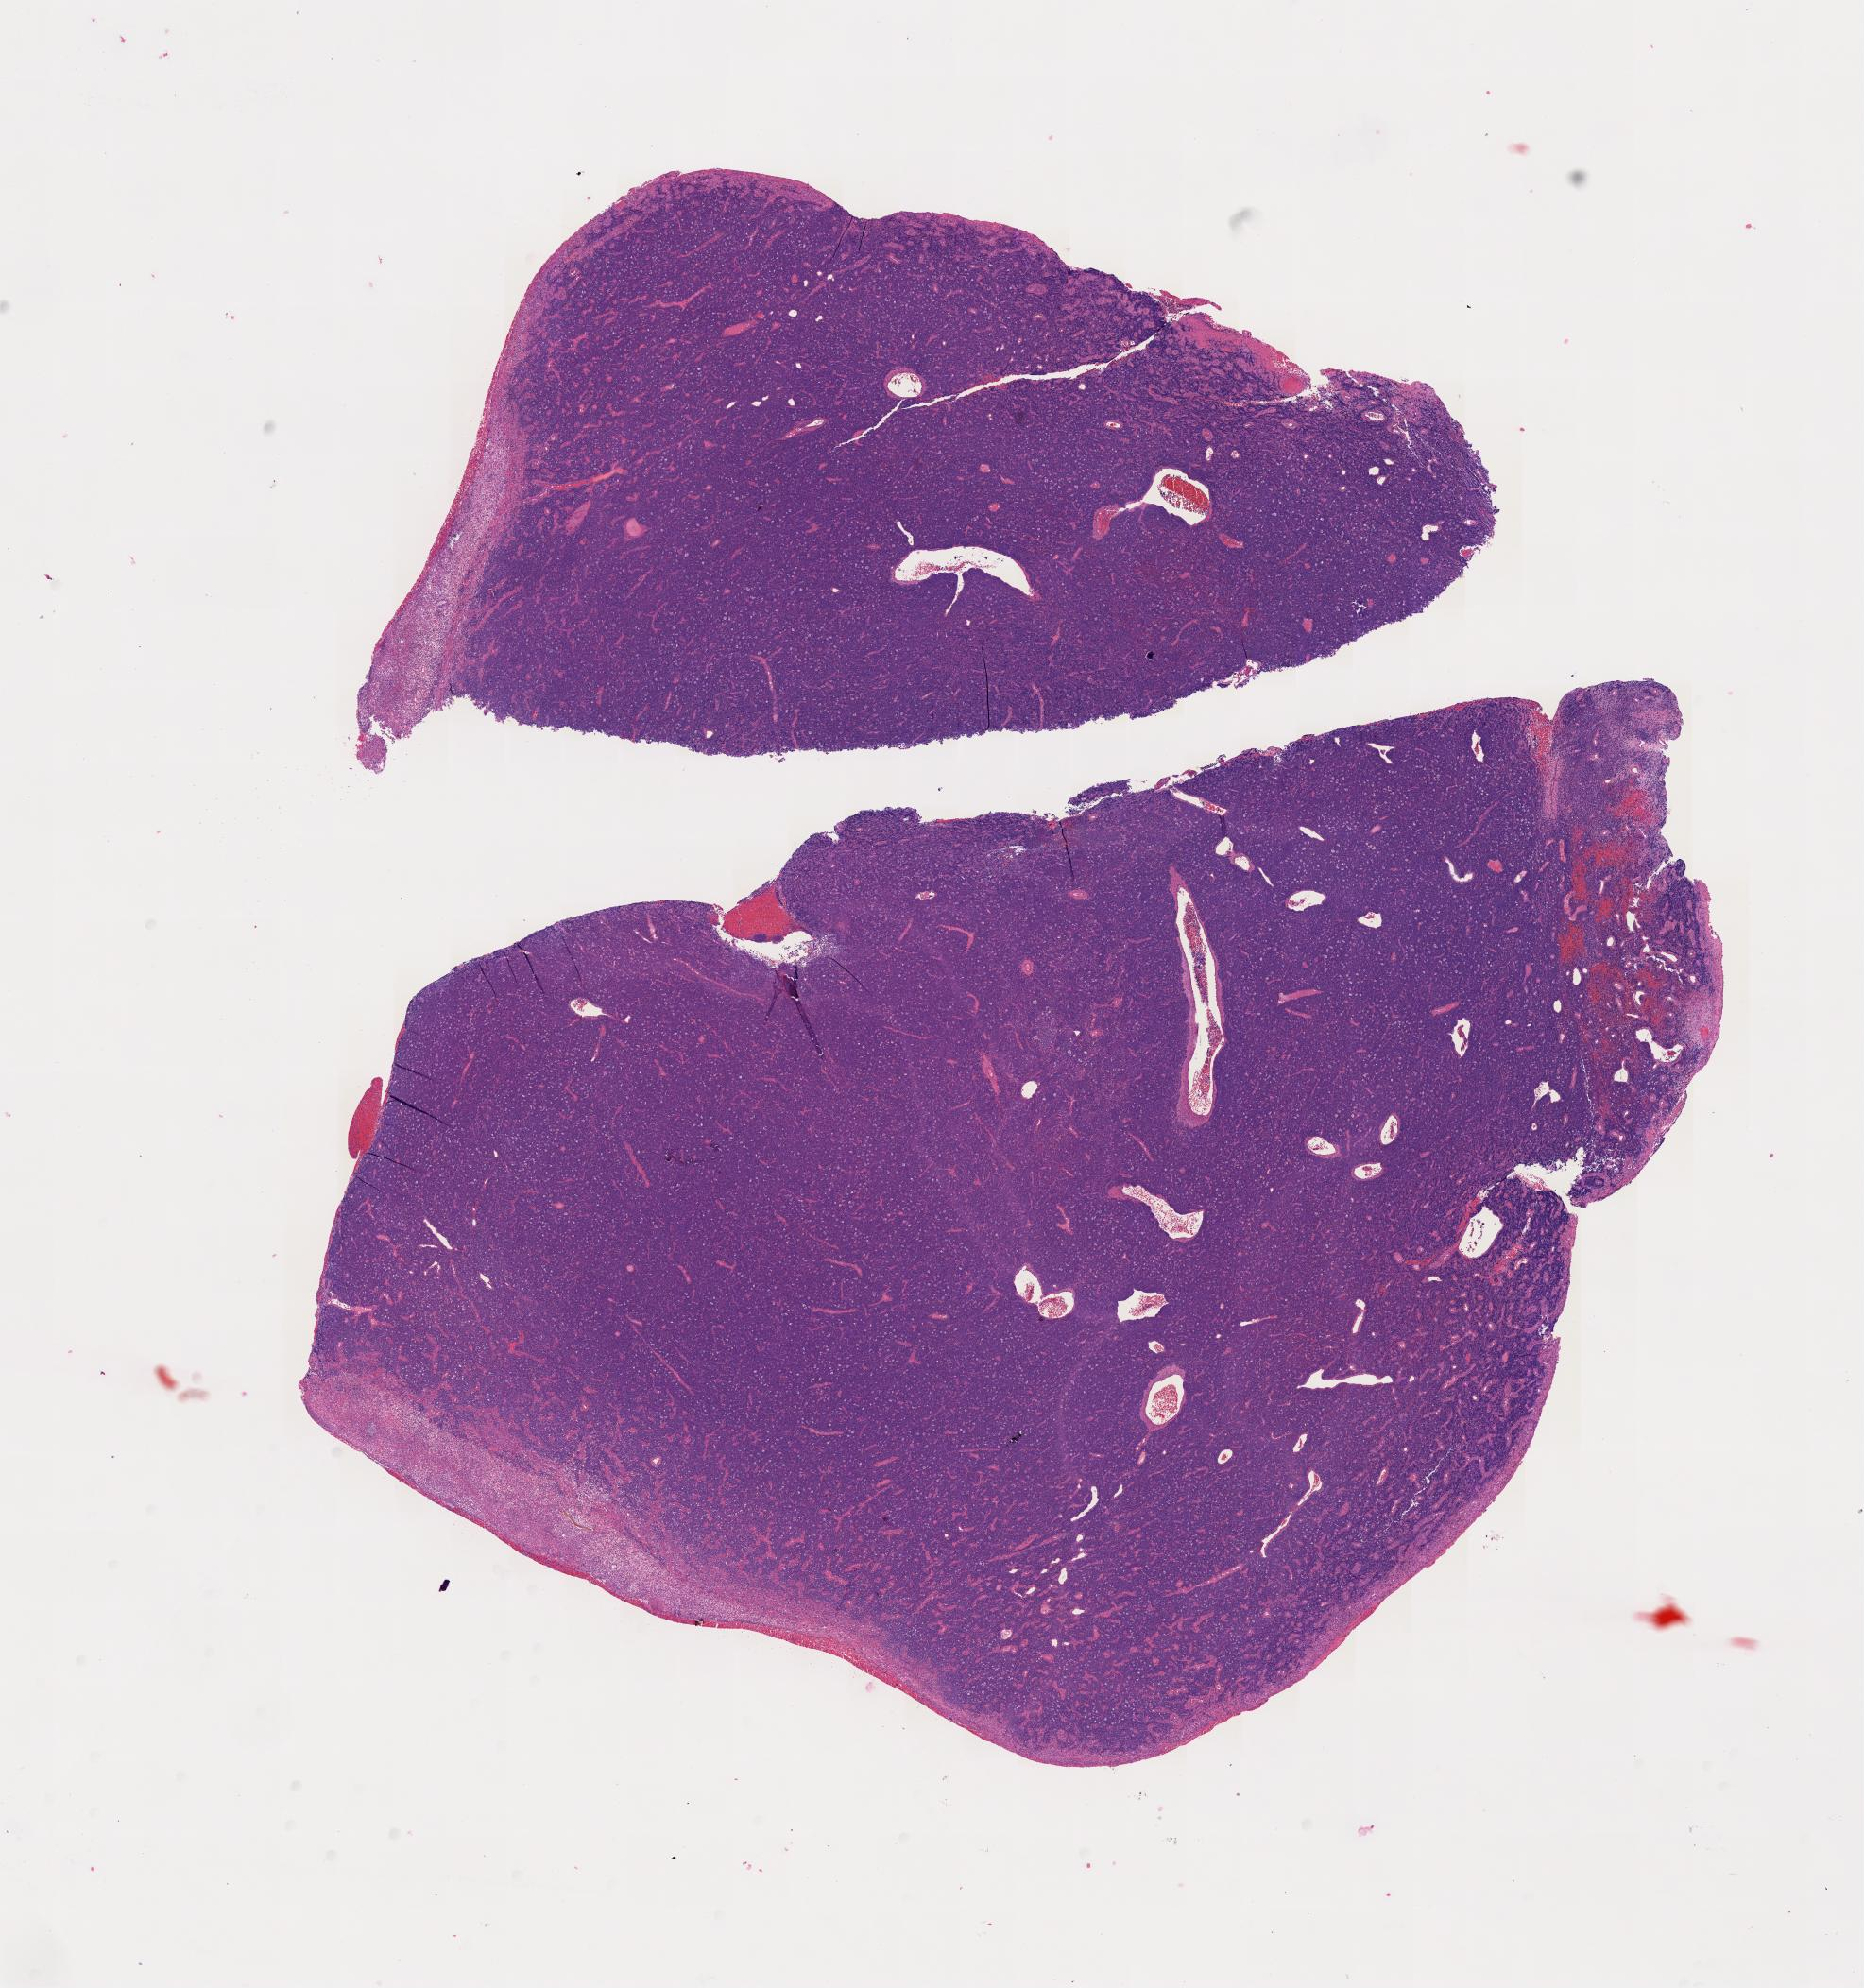
Whole-slide image, H&E stain — whole scanned area shown as a low-resolution overview; specimen: tumor tissue; site: cranium. Patient: female, age at initial diagnosis 6 years.
- histologic diagnosis: Burkitt lymphoma, NOS